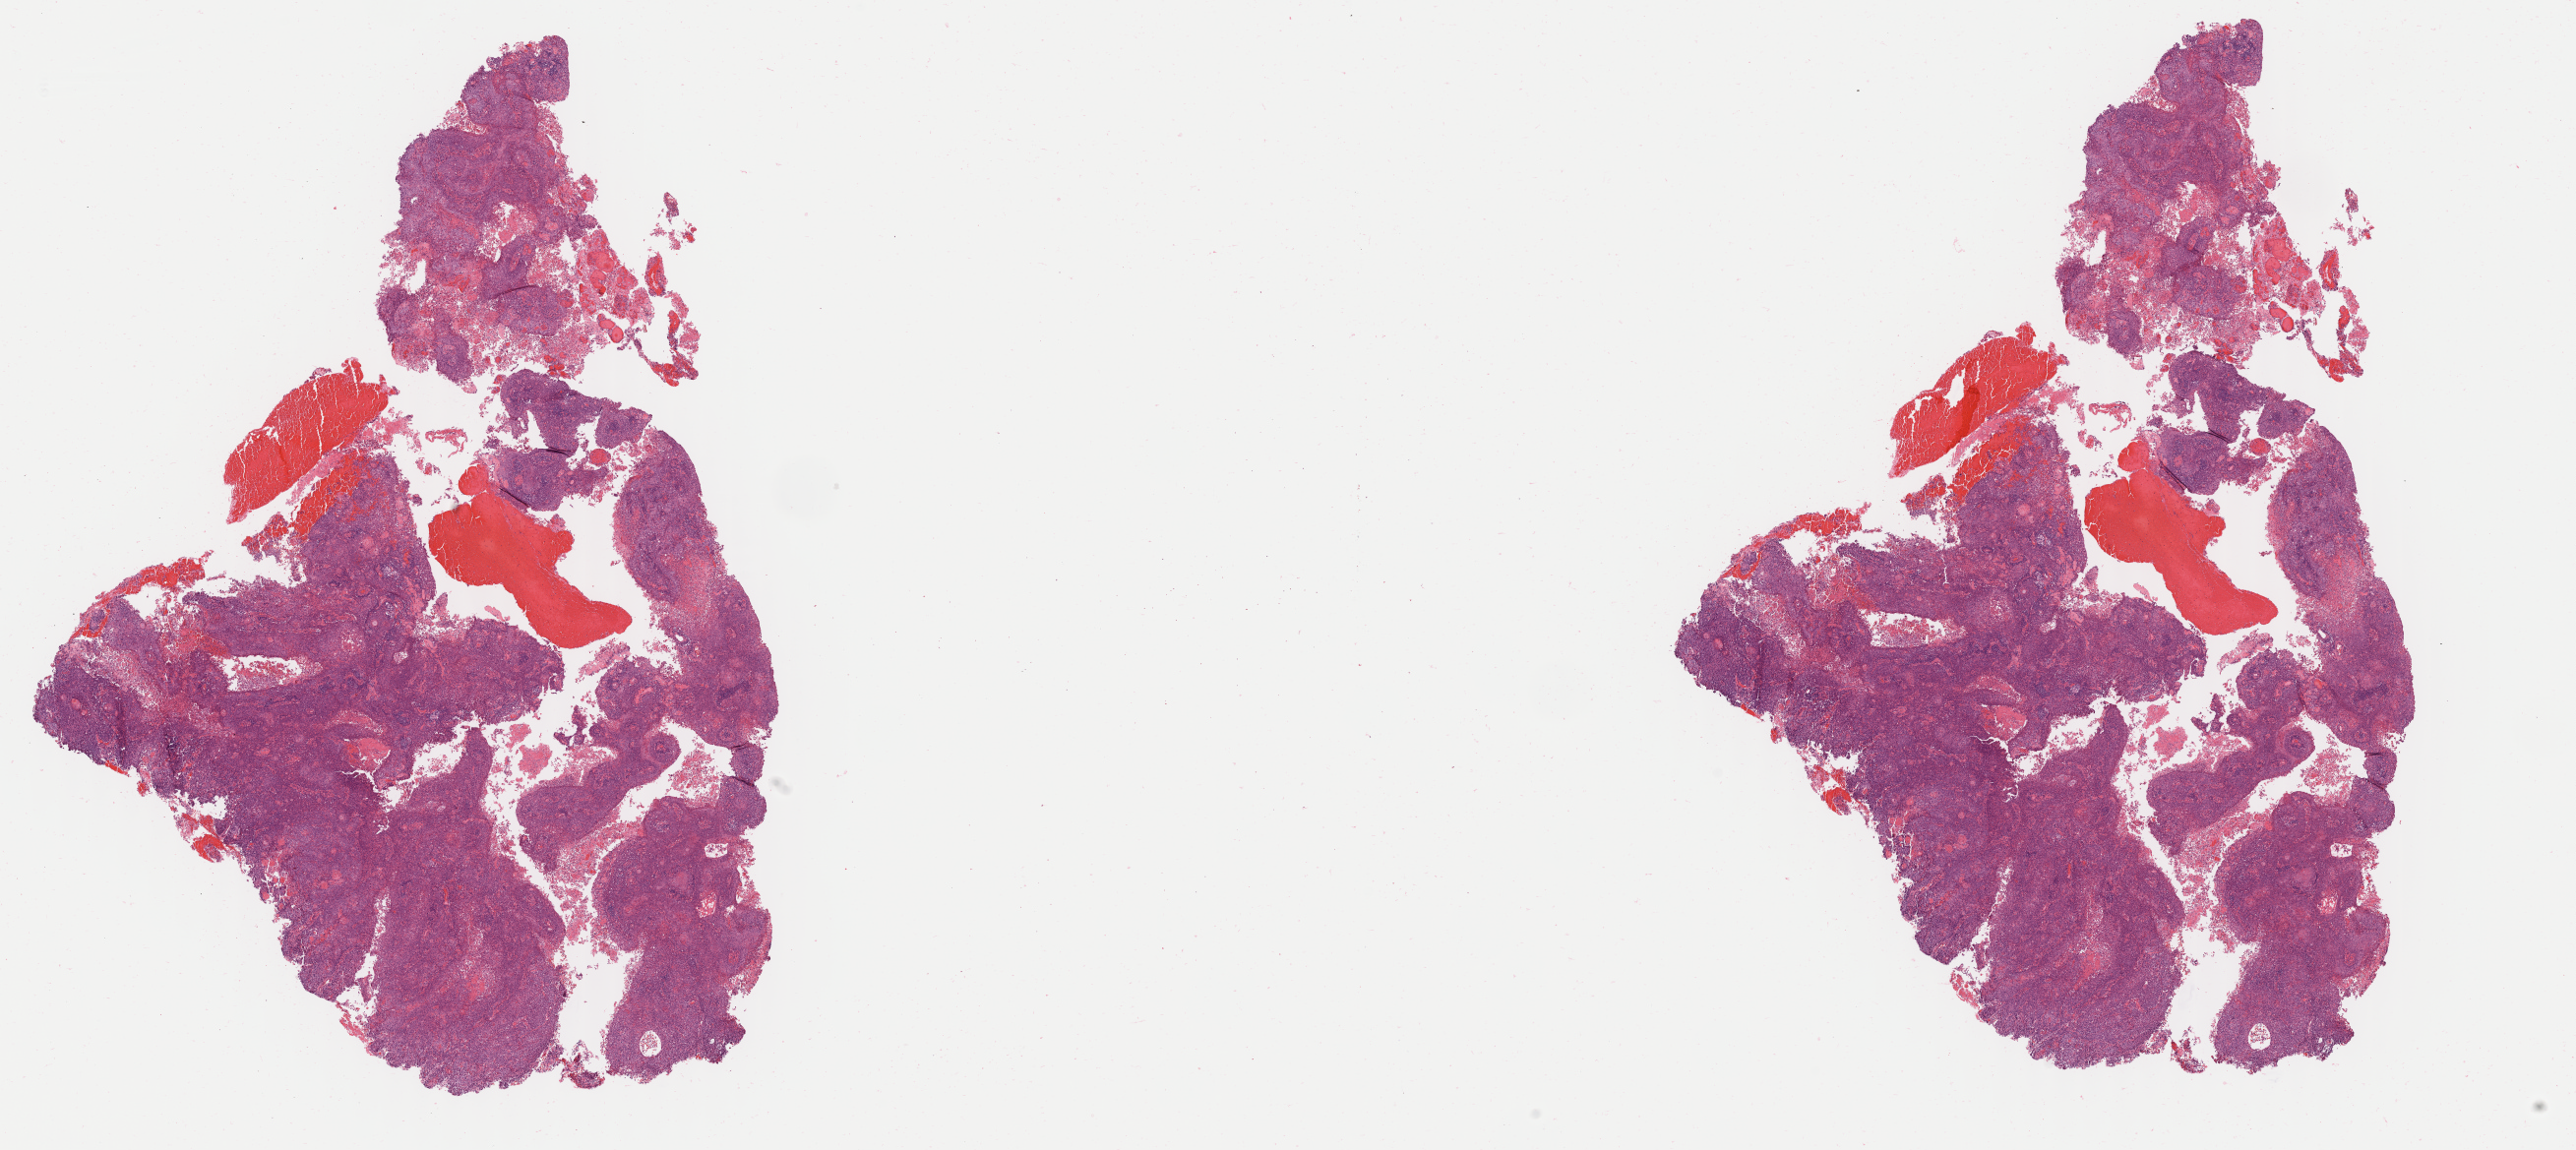
Whole-slide image, H&E stain, a low-resolution overview of the entire scanned area, about 20.8 x 9.3 mm; tumor tissue; site: cervix. Patient: female, age 45 years.
Histologic diagnosis: Squamous cell carcinoma, keratinizing, NOS.